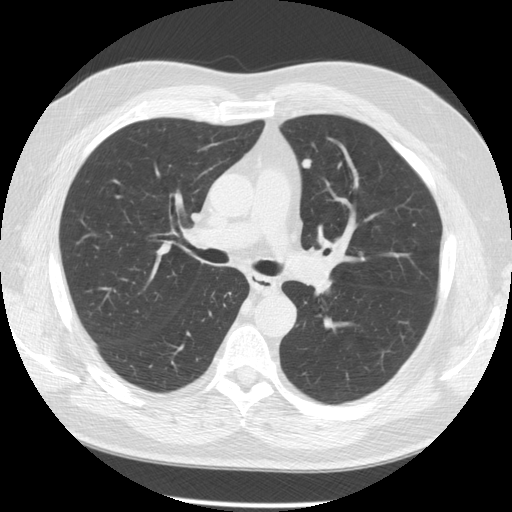
Chest CT (low-dose screening protocol), one axial image, second annual screen, lung window (W 1500 / L -600 HU), standard (soft-tissue) reconstruction kernel (STANDARD), 120 kVp, 512 × 512 image matrix, field of view 370 × 370 mm. Male participant, aged 64 years at enrolment. Former smoker at enrolment.
Lesion marked by an expert reader, bounding box (x1, y1, x2, y2) in pixels: (288, 145, 328, 182). The screening reader recorded 2 non-calcified nodules or masses ≥4 mm on this exam; which of them this box marks is not recorded. Official screen result: positive, other. Participant outcome: lung cancer diagnosed 58 days after this screen — squamous cell carcinoma, NOS, left upper lobe, poorly differentiated (G3), stage IA (AJCC 6th edition), 14 mm at pathology.